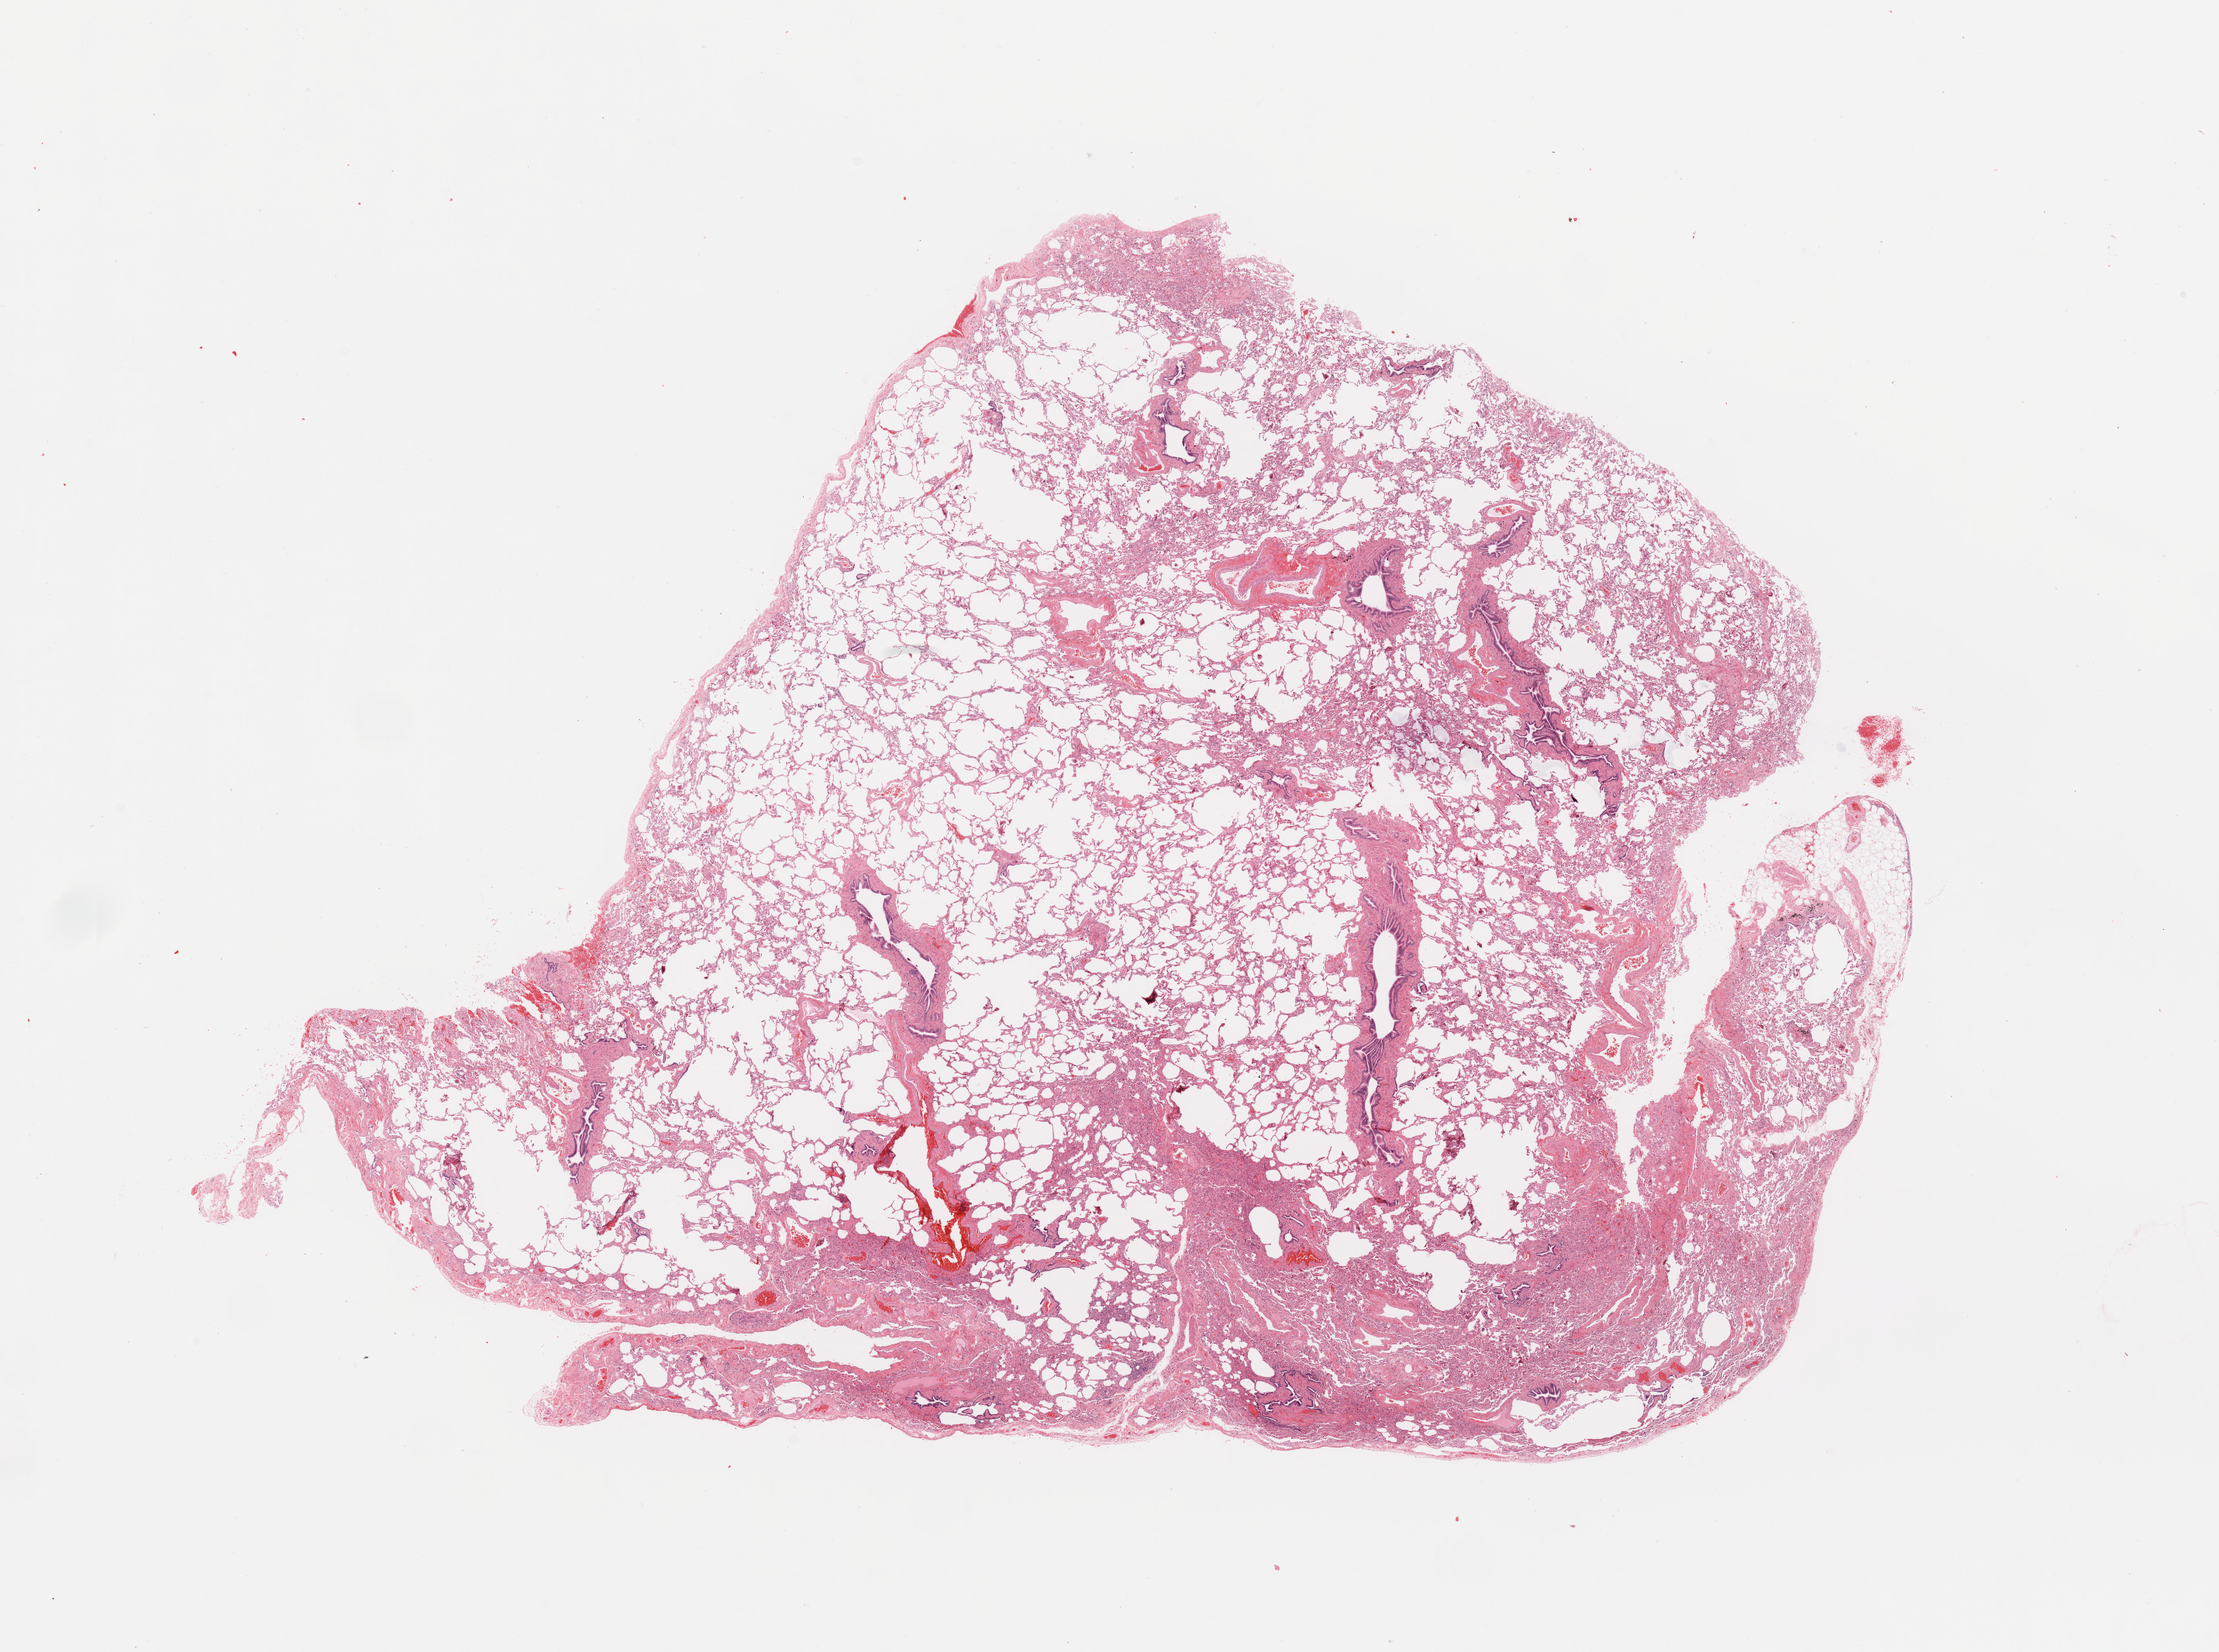
Whole-slide histology image, H&E — shown as a low-resolution overview of the whole scanned area (about 22.6 x 16.9 mm, slide scanned at 20x); normal (non-tumour) tissue sample, sampled site: lung. 59-year-old female patient.
• this section: normal (non-tumour) tissue from the same patient
• patient diagnosis: Adenocarcinoma, NOS